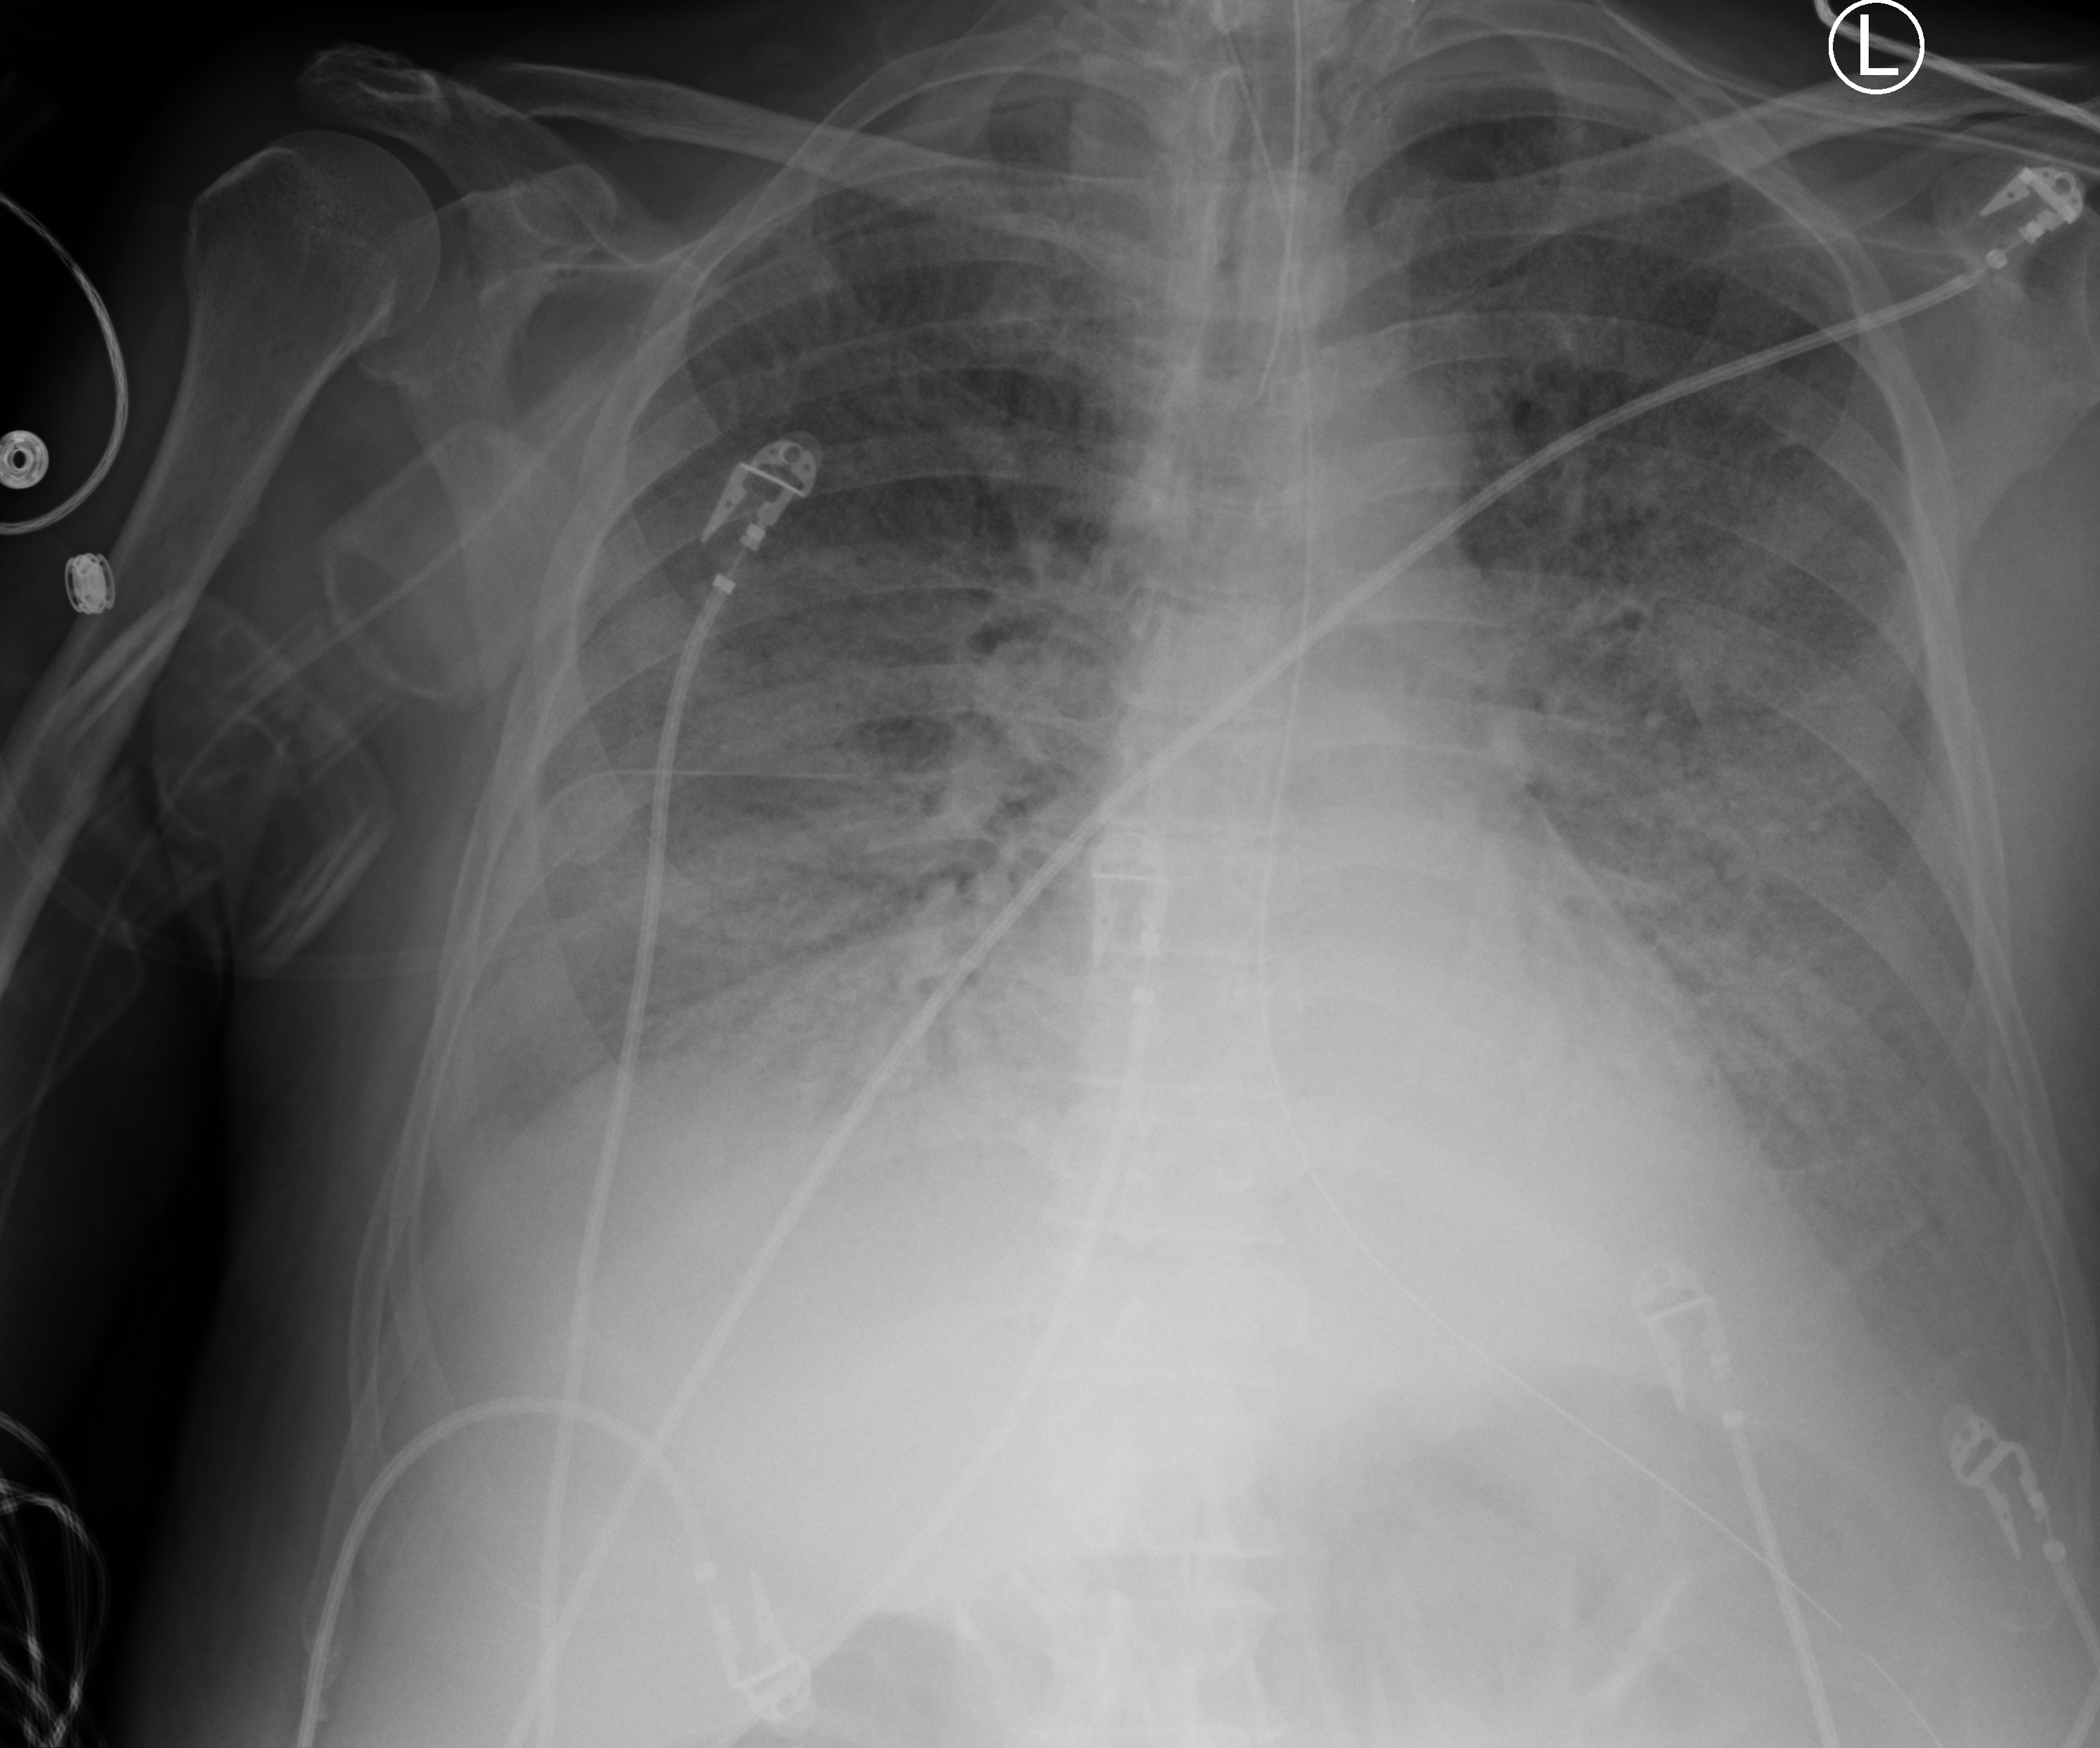
Chest X-ray (portable), anteroposterior (AP) projection. Patient hospitalised with COVID-19; male, aged 60–74 years.
Hospital-stay facts (about this admission, not read from this image; timing relative to this image not recorded):
- admitted to intensive care during this hospital stay: yes
- mechanically ventilated during this hospital stay: yes